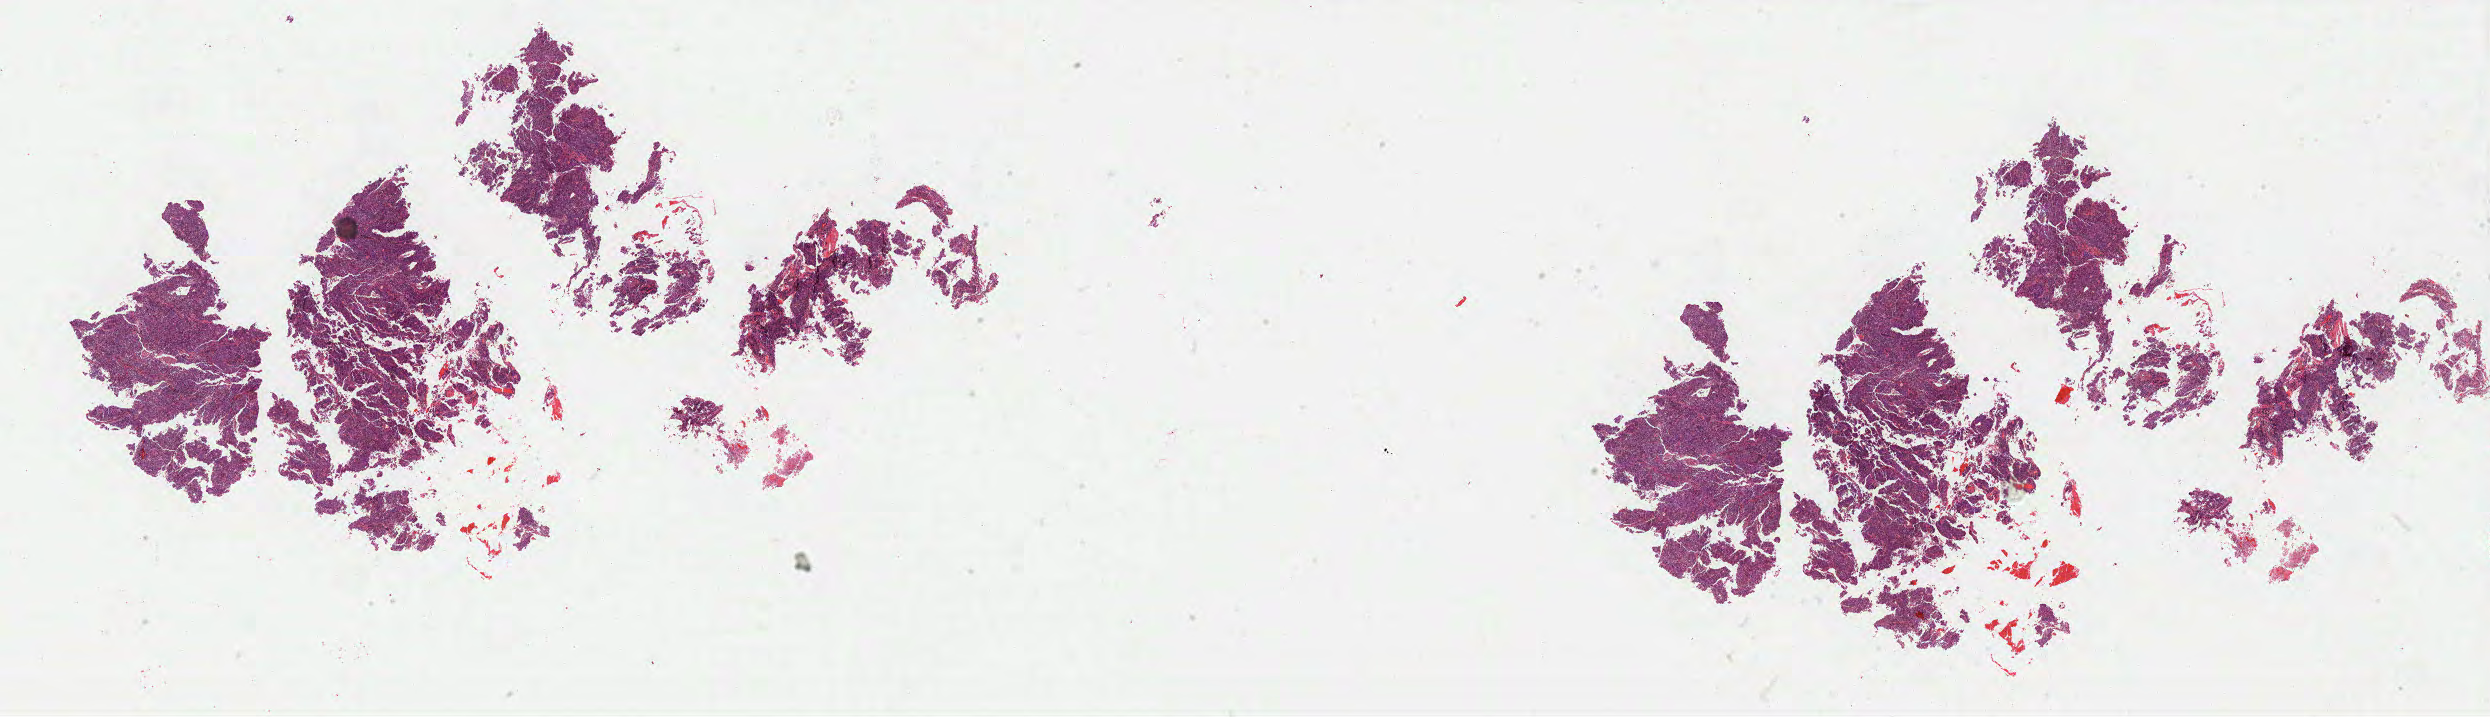
Digitized H&E tissue section (whole slide) — whole scanned area (about 39.9 x 11.5 mm, slide scanned at 40x) shown as a low-resolution overview, formalin-fixed paraffin-embedded (FFPE) diagnostic section, cervix, primary tumour sample. Patient: female, age at initial diagnosis 44 years. Histologic grade: G3 (poorly differentiated).
FIGO stage: IB2. Histologic diagnosis: Squamous cell carcinoma, NOS (cervix uteri).